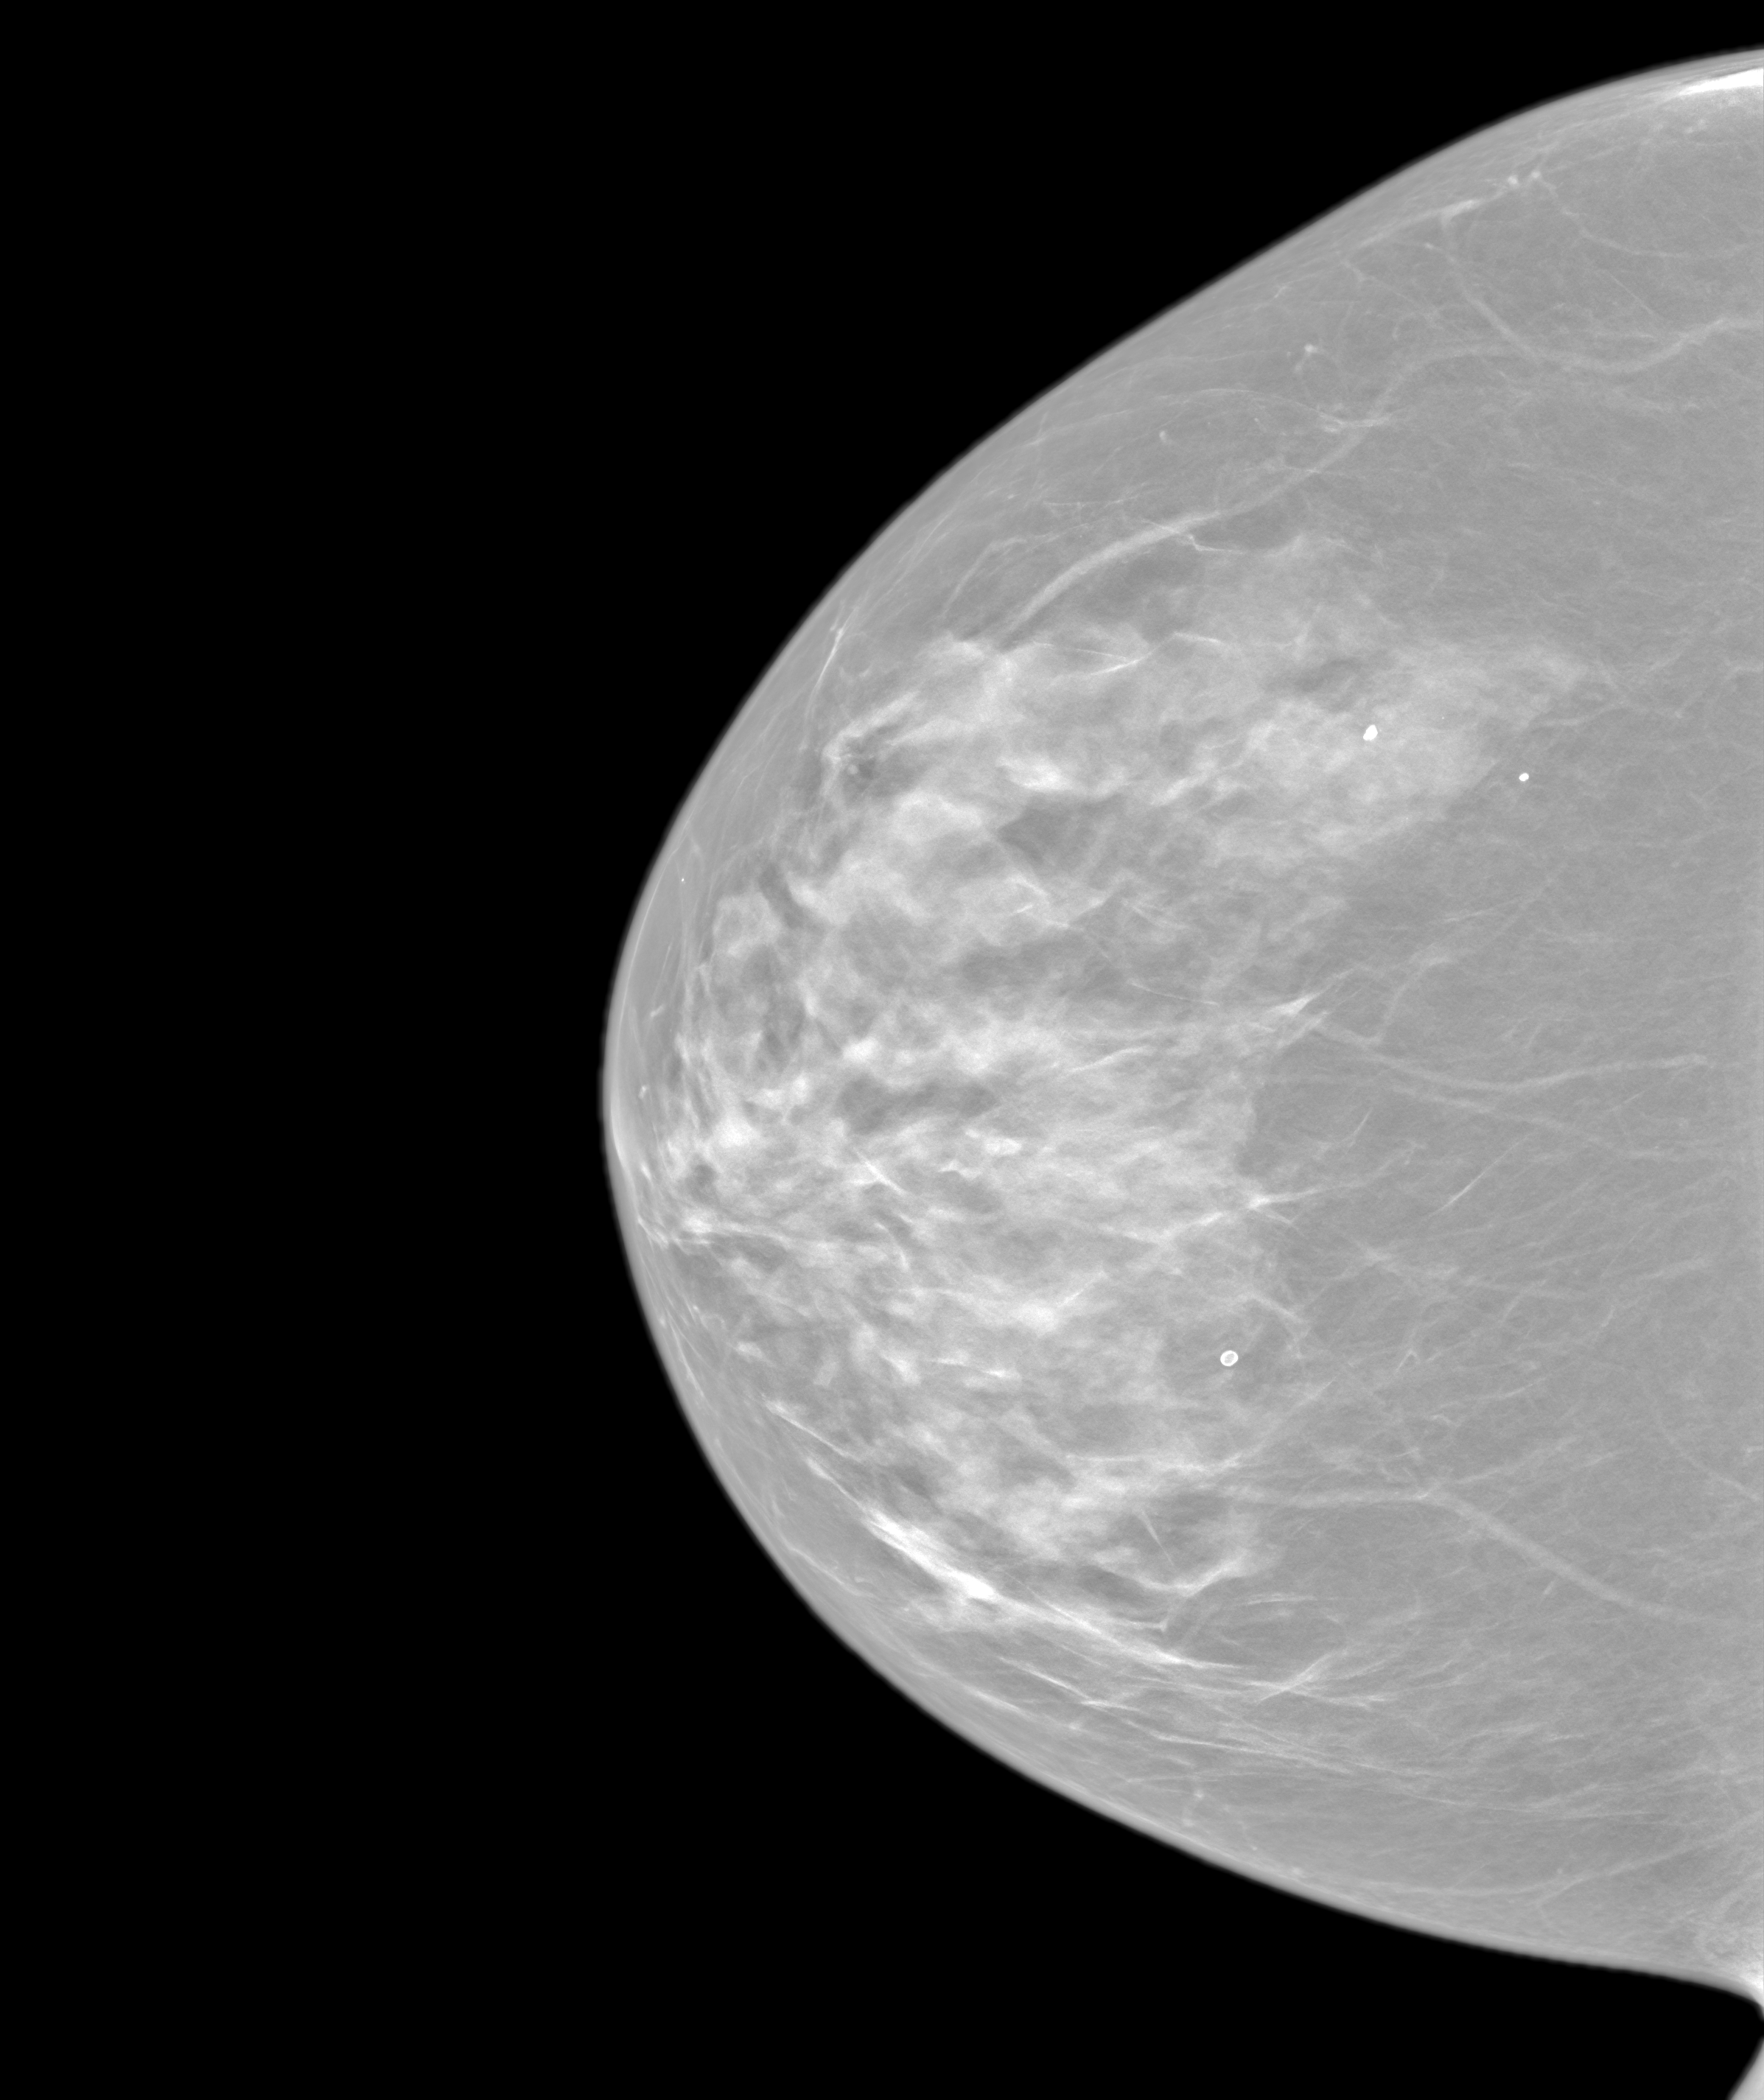
Annual screening mammography examination. Female patient, age 66 years.
Image type: synthesized 2-D view from tomosynthesis. Breast: right. Projection: CC view.